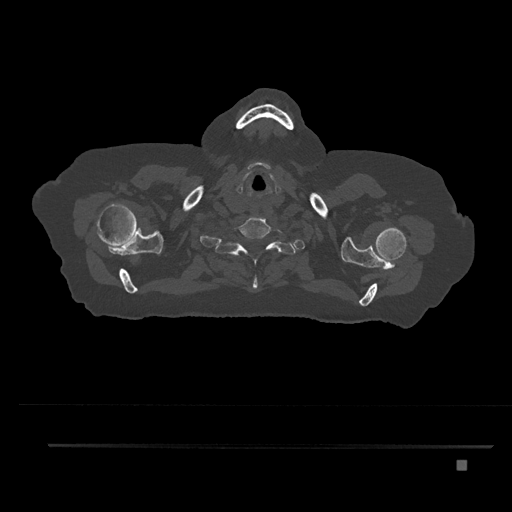
CT including the spine, one axial slice. Reconstruction kernel Br40s/3. 120 kVp. Bone window (W 1800 / L 400 HU). 0.5 mm slice thickness. 512 × 512 image matrix, field of view 437 × 437 mm. Female patient, age 76 years. From the clinical record (not read from this slice): primary cancer: lung; vertebrae with lytic lesions (as recorded): T11, L3.
Structures marked on this image (semi-automatically segmented with operator editing):
- T1 vertebra: bounding box (x1, y1, x2, y2) in pixels: (223, 237, 284, 289)